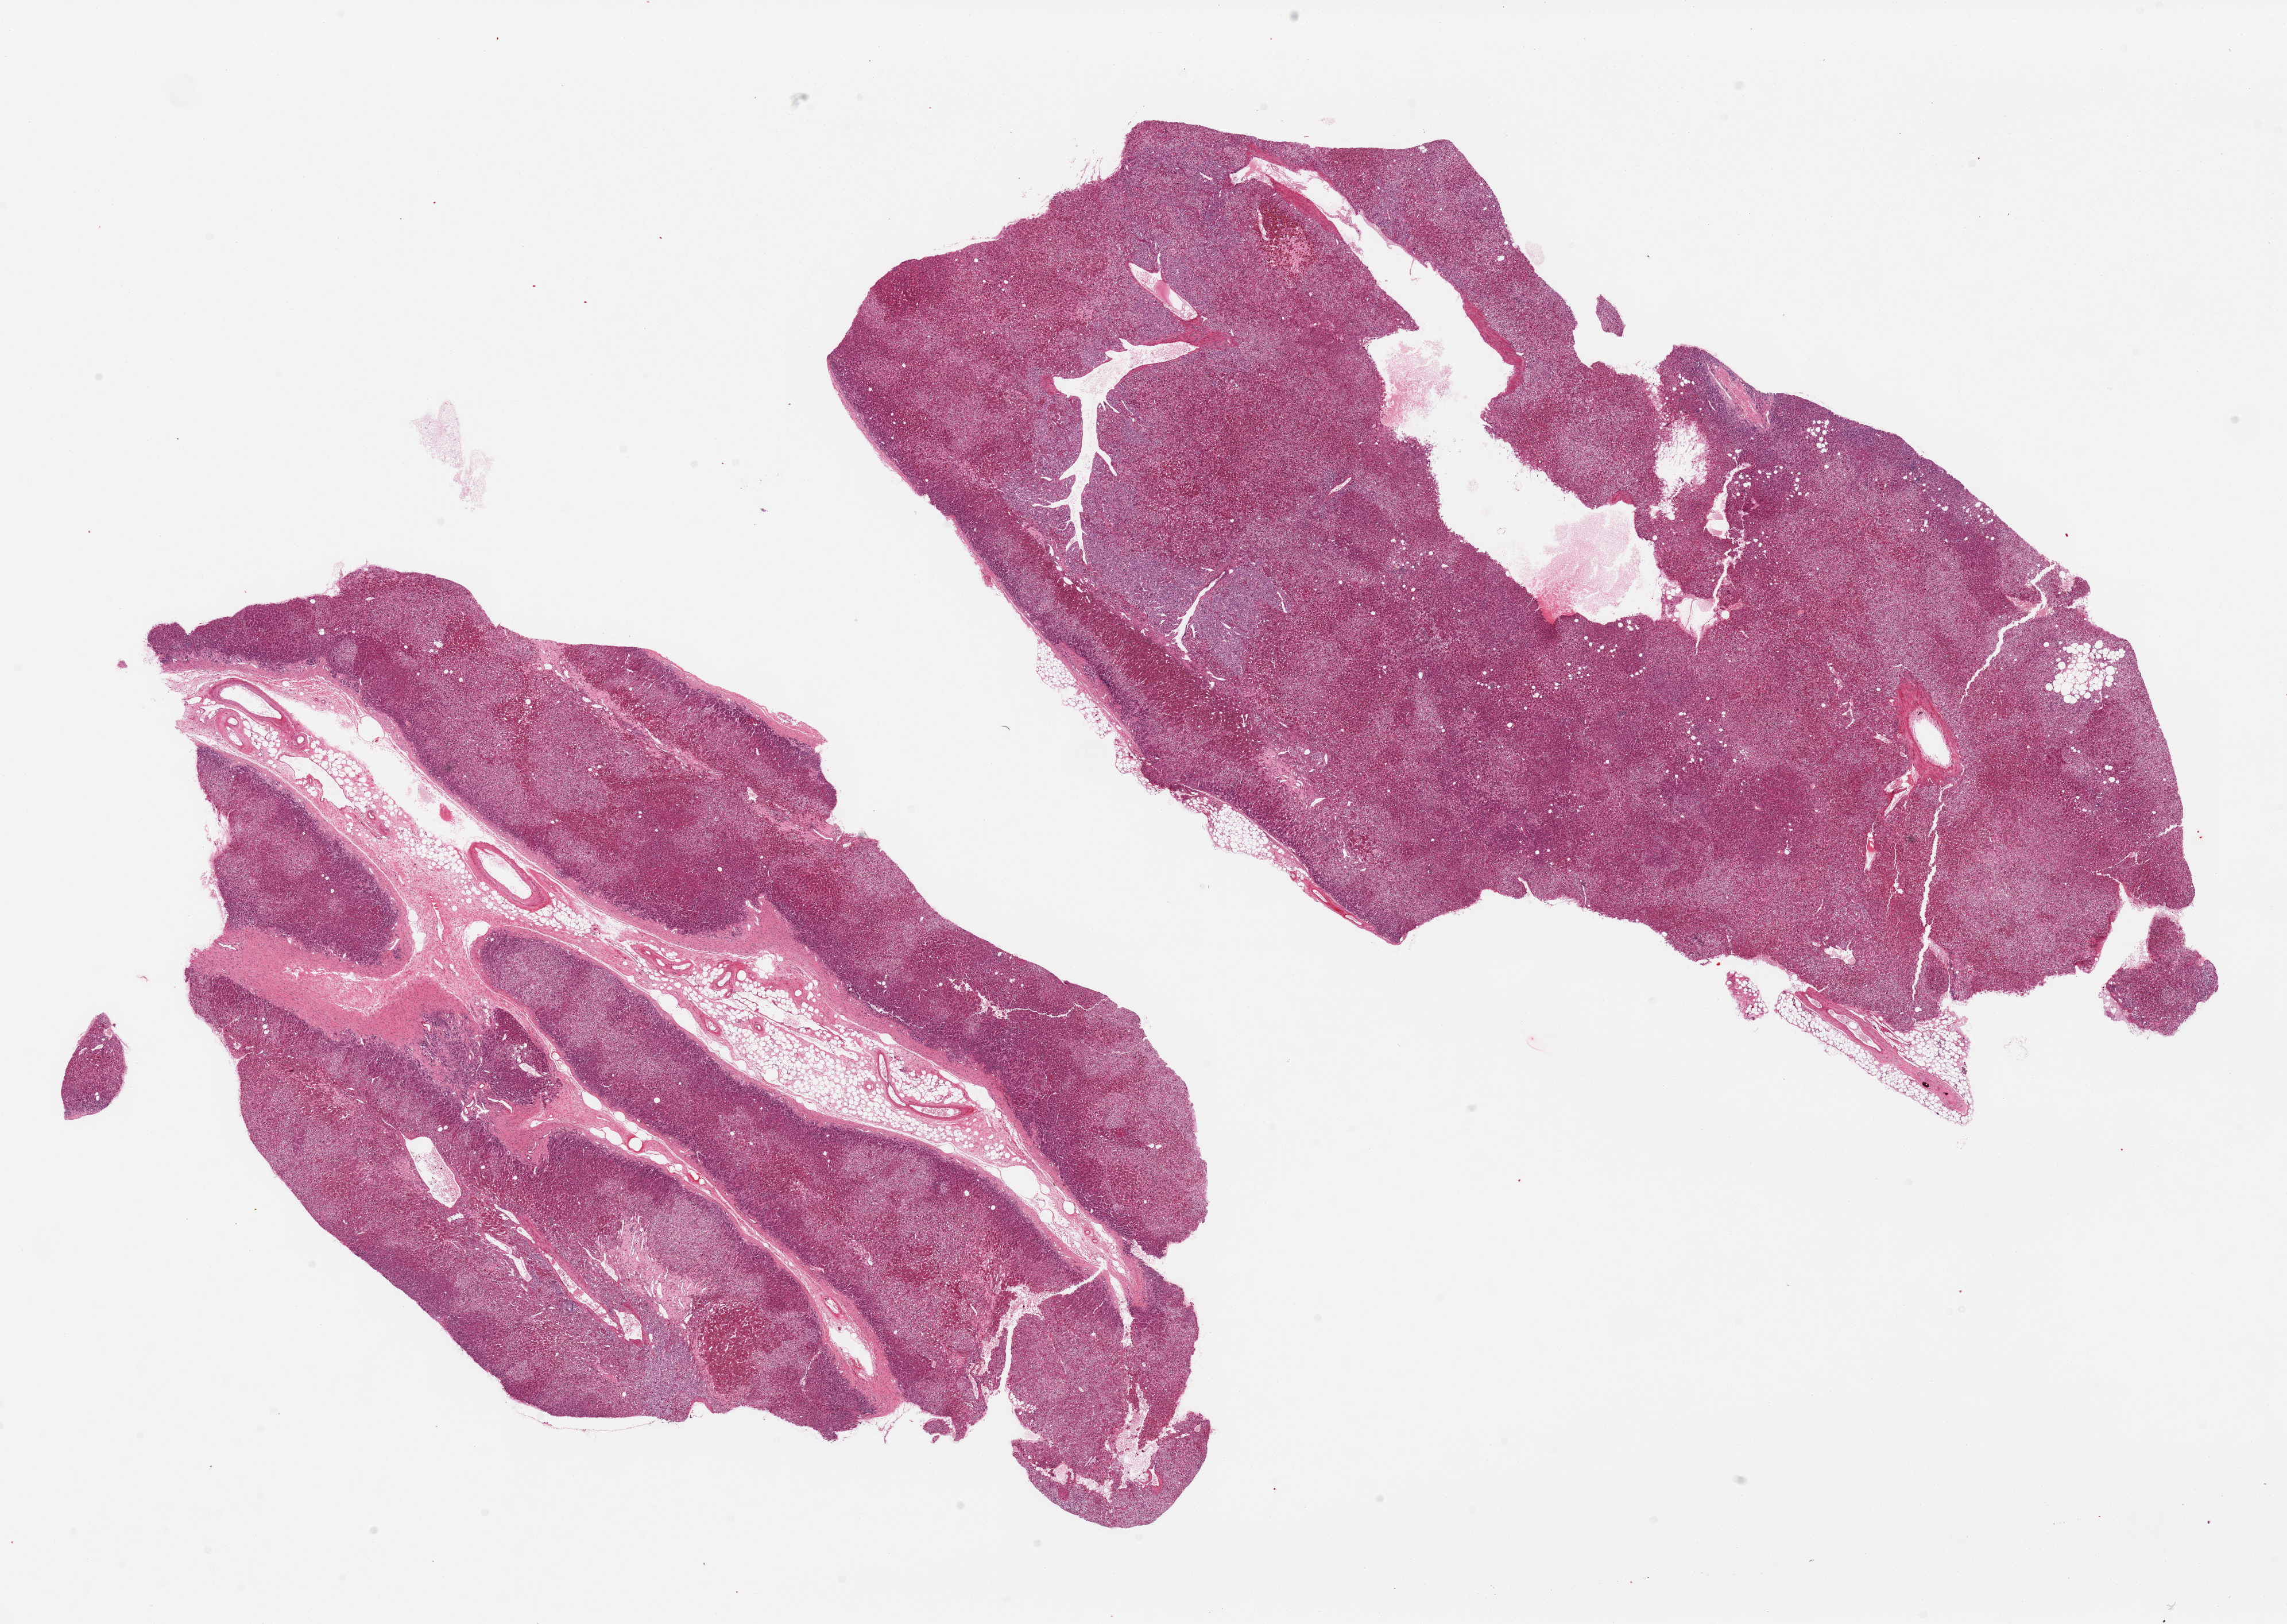
Digitized H&E-stained section — a low-resolution overview of the entire scanned area, about 31.5 x 22.4 mm, PAXgene-fixed, paraffin-embedded tissue, section of adrenal gland (target tissue), donor tissue sample.
Reviewer comment on this tissue sample: 2 pieces; 15% fat in one.